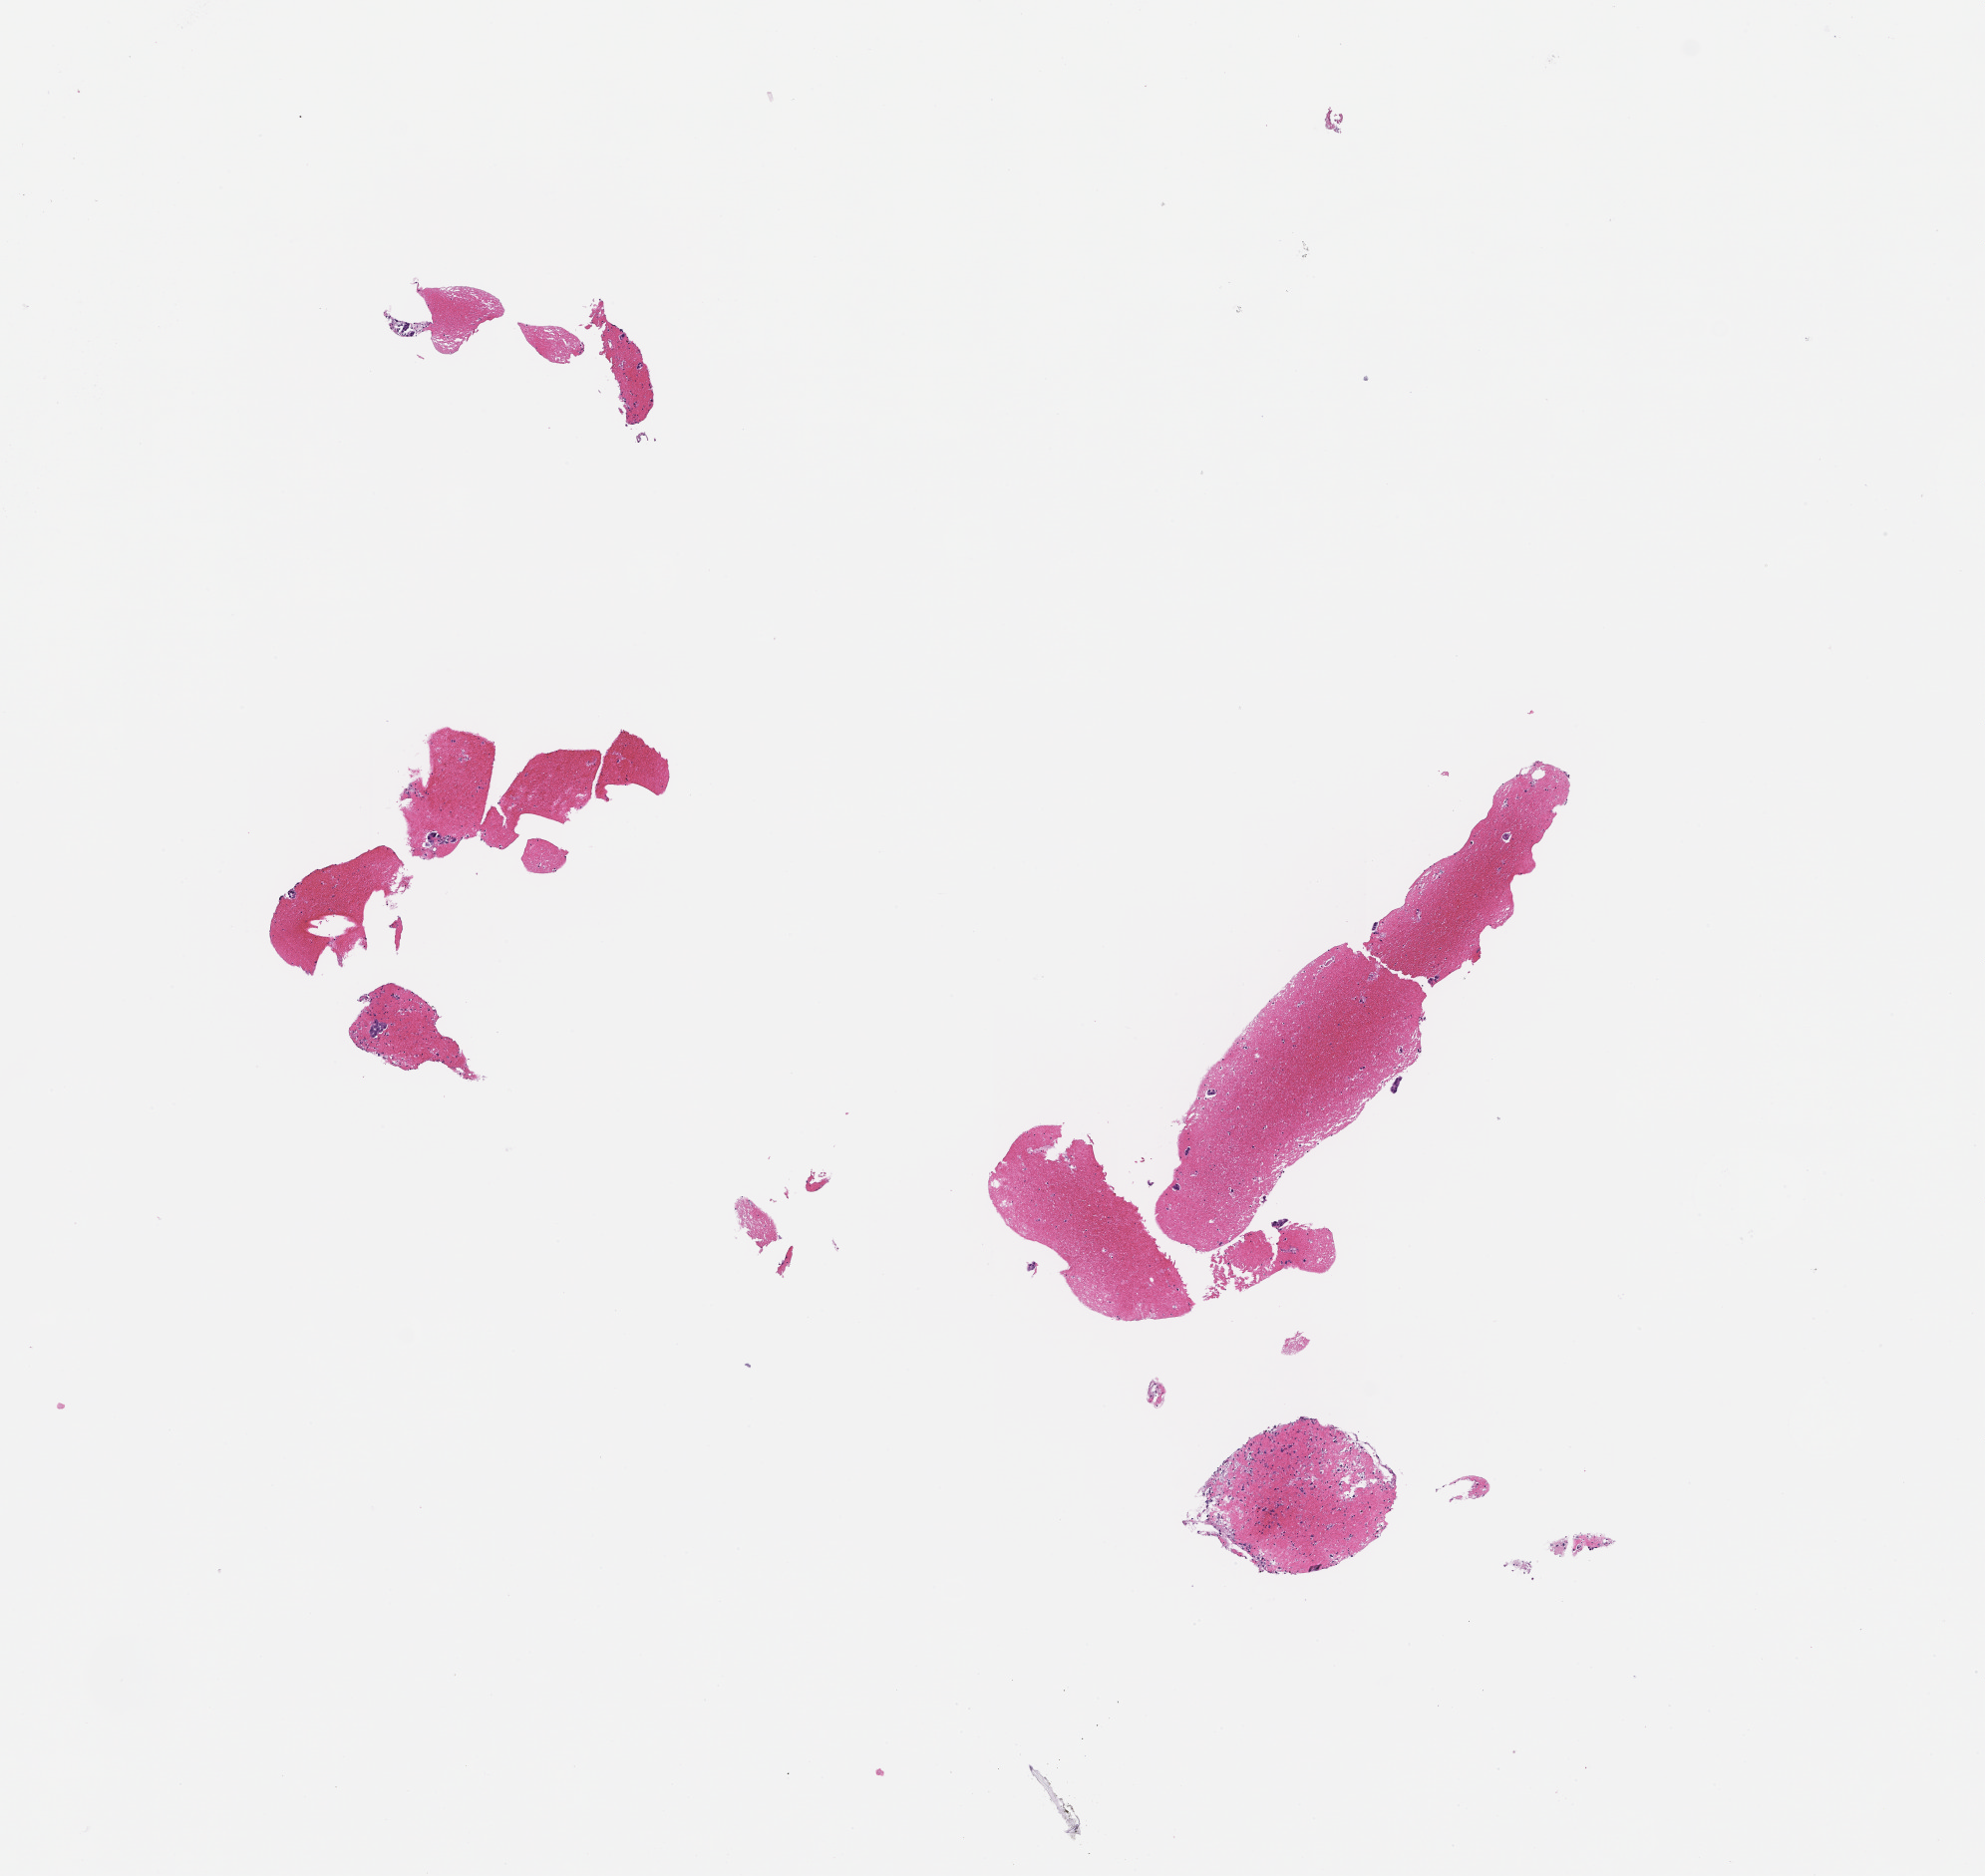
Digitized H&E-stained section, a low-resolution overview of the entire scanned area, about 8.0 x 7.6 mm. Formalin-fixed paraffin-embedded section. Tissue site: lung. Specimen time point: archival tissue. Male patient.
This section: primary tumour tissue. Diagnosis: Non-Small Cell Lung Carcinoma.